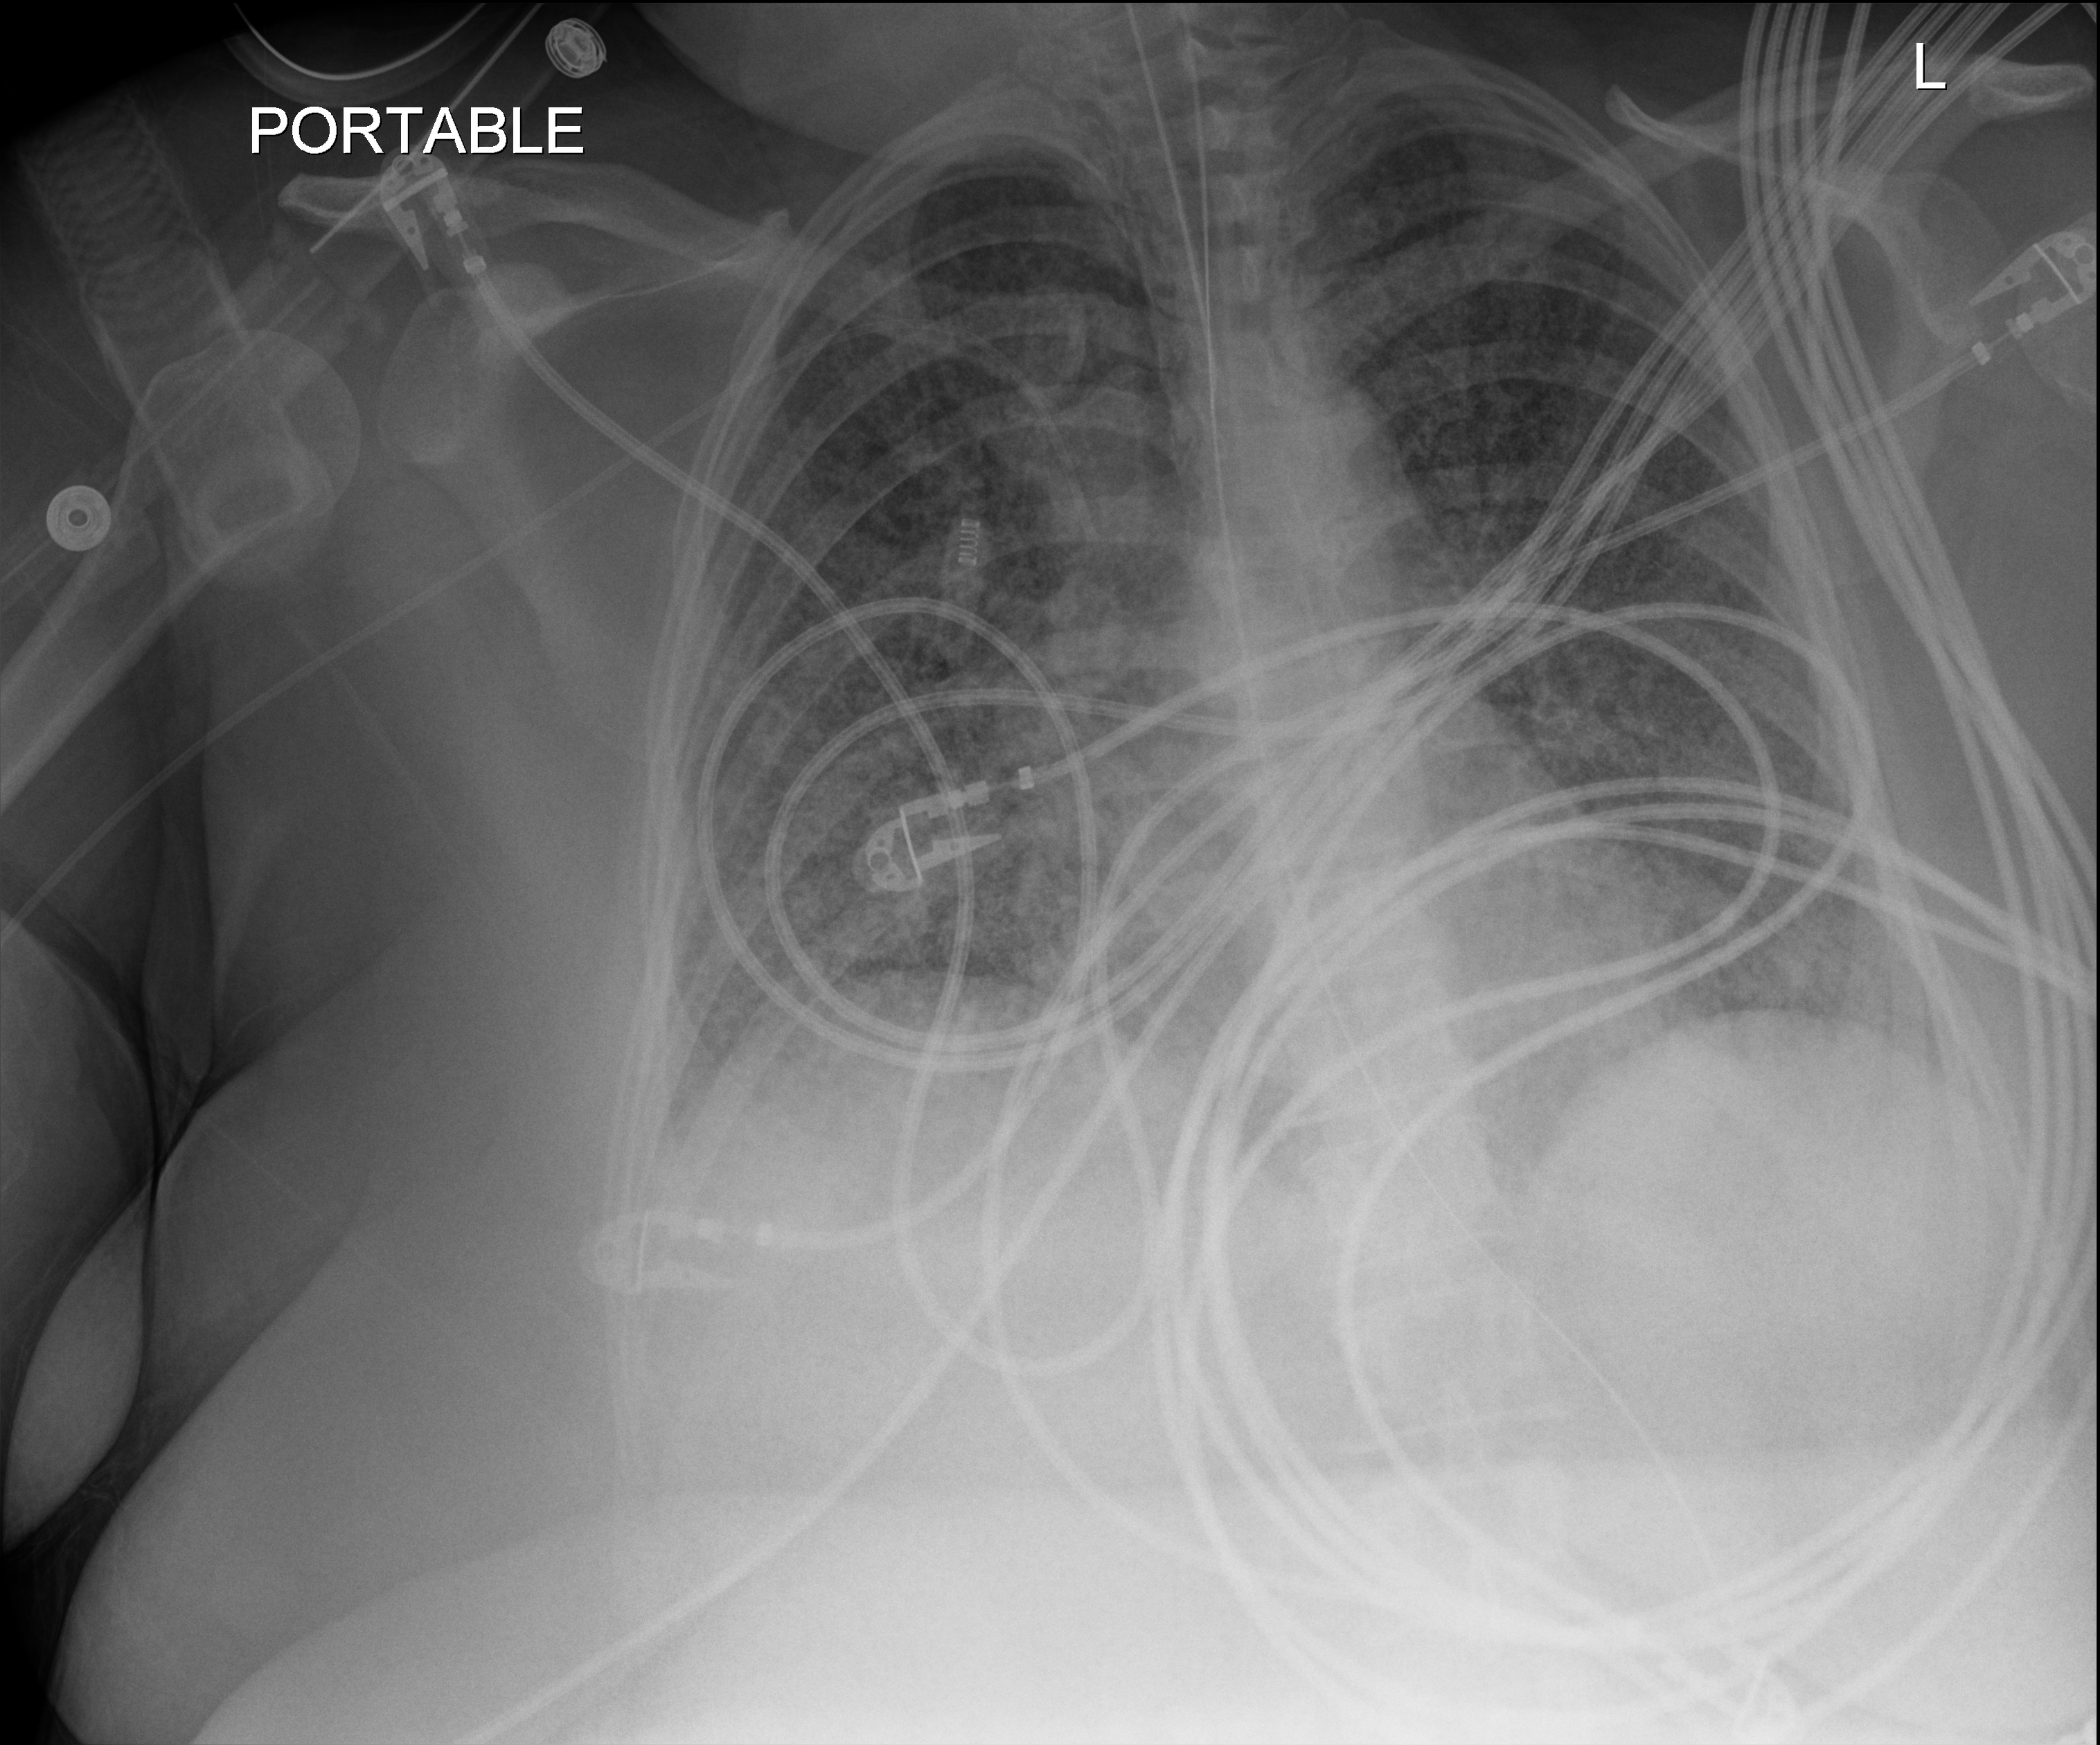
Chest X-ray (portable), anteroposterior (AP) projection. Female patient hospitalised with COVID-19, age 18–59 years.
Admission-level facts for this patient (not findings on this image; timing relative to this image not recorded): mechanically ventilated during this hospital stay: yes; smoking status (admission record): never.